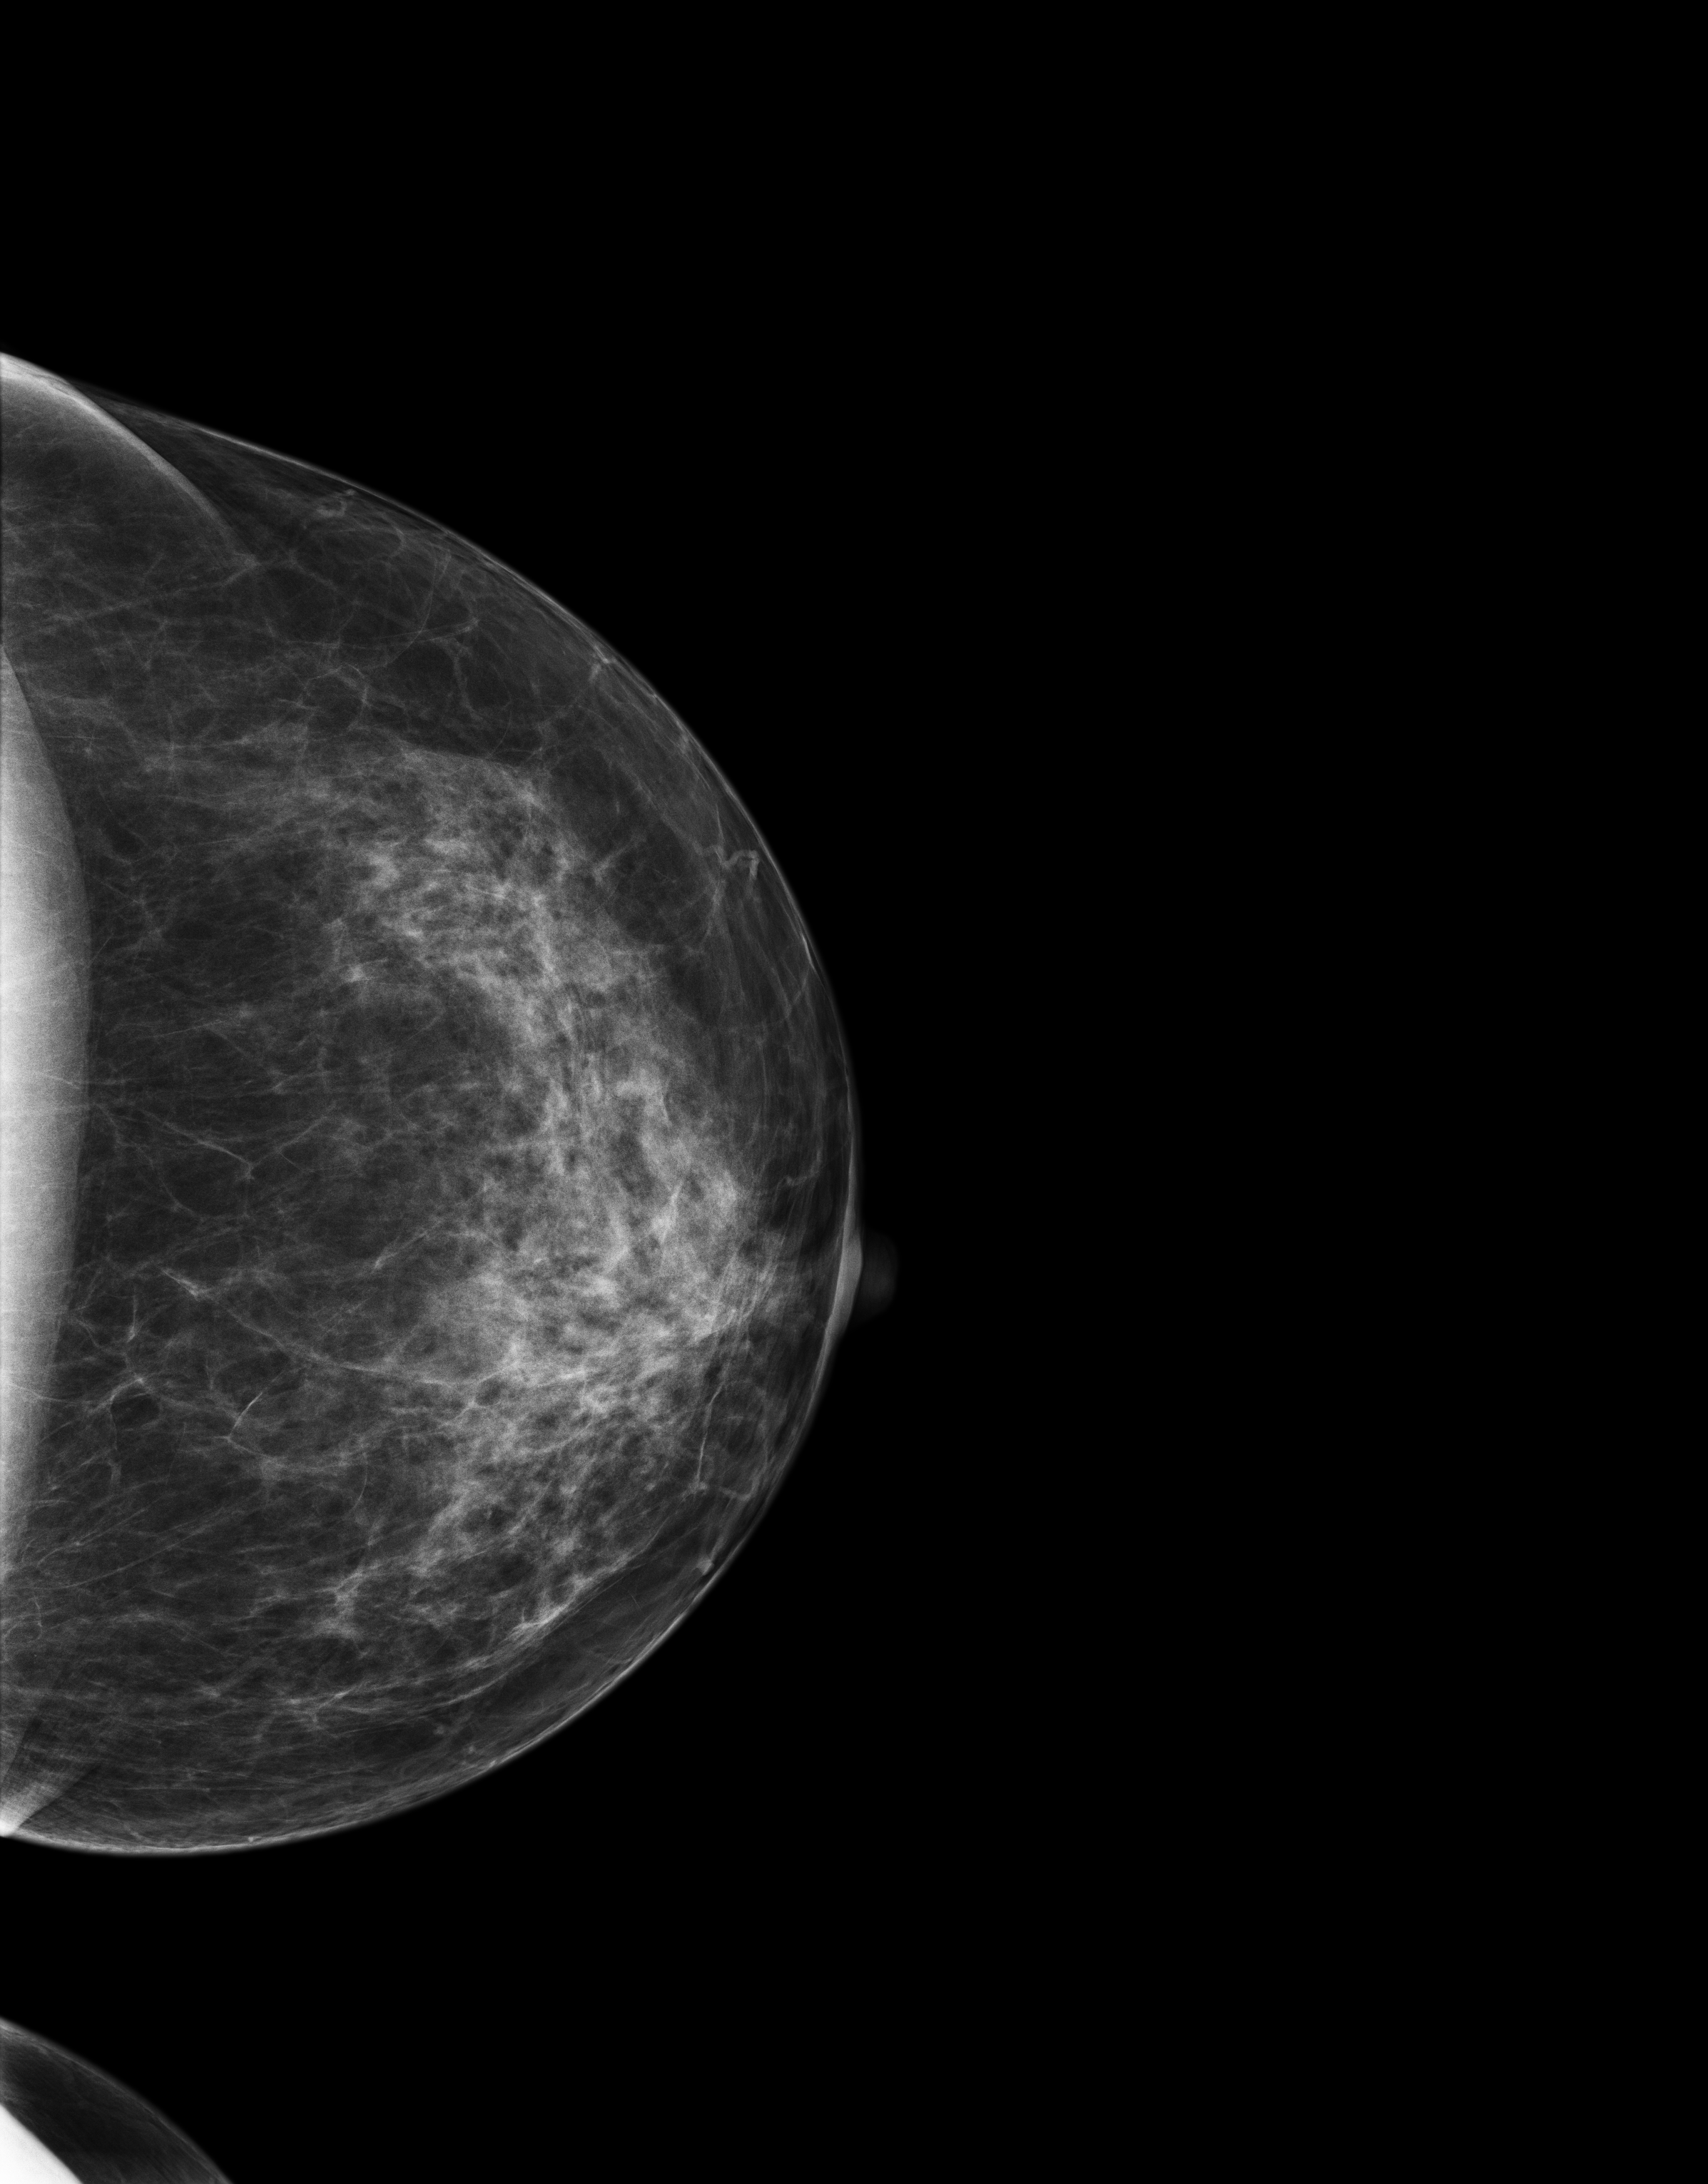
Annual screening mammography examination. Patient: female, 54 years.
Image type: full-field digital mammogram. Breast: left. Projection: cranio-caudal projection.